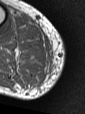
MRI of an extremity soft-tissue mass, one axial slice; position 36 of 47 along the scan axis; MR volume resampled by the dataset authors to the PET/CT grid (not the native acquisition matrix); 85 × 114 image matrix, field of view 83 × 111 mm. Male patient. Case-level facts recorded for this patient, not image findings: histological type: pleiomorphic liposarcoma; grade: high; site of the primary tumour: right calf.
Outlined on this slice (expert contour drawn on MRI and transferred to this co-registered scan by the dataset authors):
- gross tumour volume including surrounding oedema: bounding box [x1, y1, x2, y2] px = [43, 41, 48, 51]